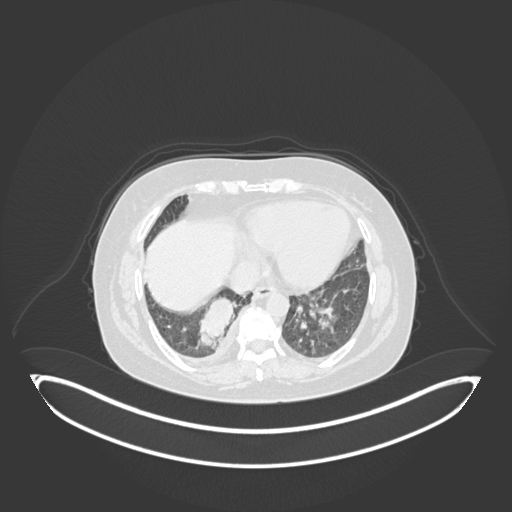
Chest CT, one axial slice. Slice 42 of 231 in the series (ordered by position). 120 kVp. Lung window (W 1500 / L -600 HU). 1 mm slice thickness. 512 × 512 image matrix, field of view 500 × 500 mm. Female patient, age 56 years. Case-level facts recorded for this patient, not image findings: clinical TNM (as recorded): T2b N1 M0.
Annotated regions visible in this slice (bounding box drawn by a radiologist):
- lung tumour (recorded histology: small cell carcinoma): box from (x=196, y=296) to (x=238, y=350) px